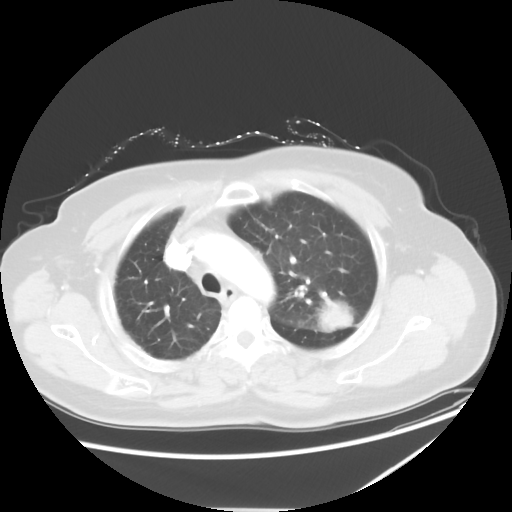
Chest CT, one axial slice. Slice 41 of 54 in the series (ordered by position). Reconstruction kernel STANDARD. 120 kVp. Lung window (W 1500 / L -600 HU). 5 mm slice thickness. 512 × 512 image matrix, field of view 384 × 384 mm. Patient: female, 61 years. Case-level facts recorded for this patient, not image findings: clinical TNM (as recorded): T1c N3 M1.
Structures marked on this image (bounding box drawn by a radiologist):
- lung tumour (recorded histology: adenocarcinoma): bounding box [x1, y1, x2, y2] px = [314, 292, 358, 337]